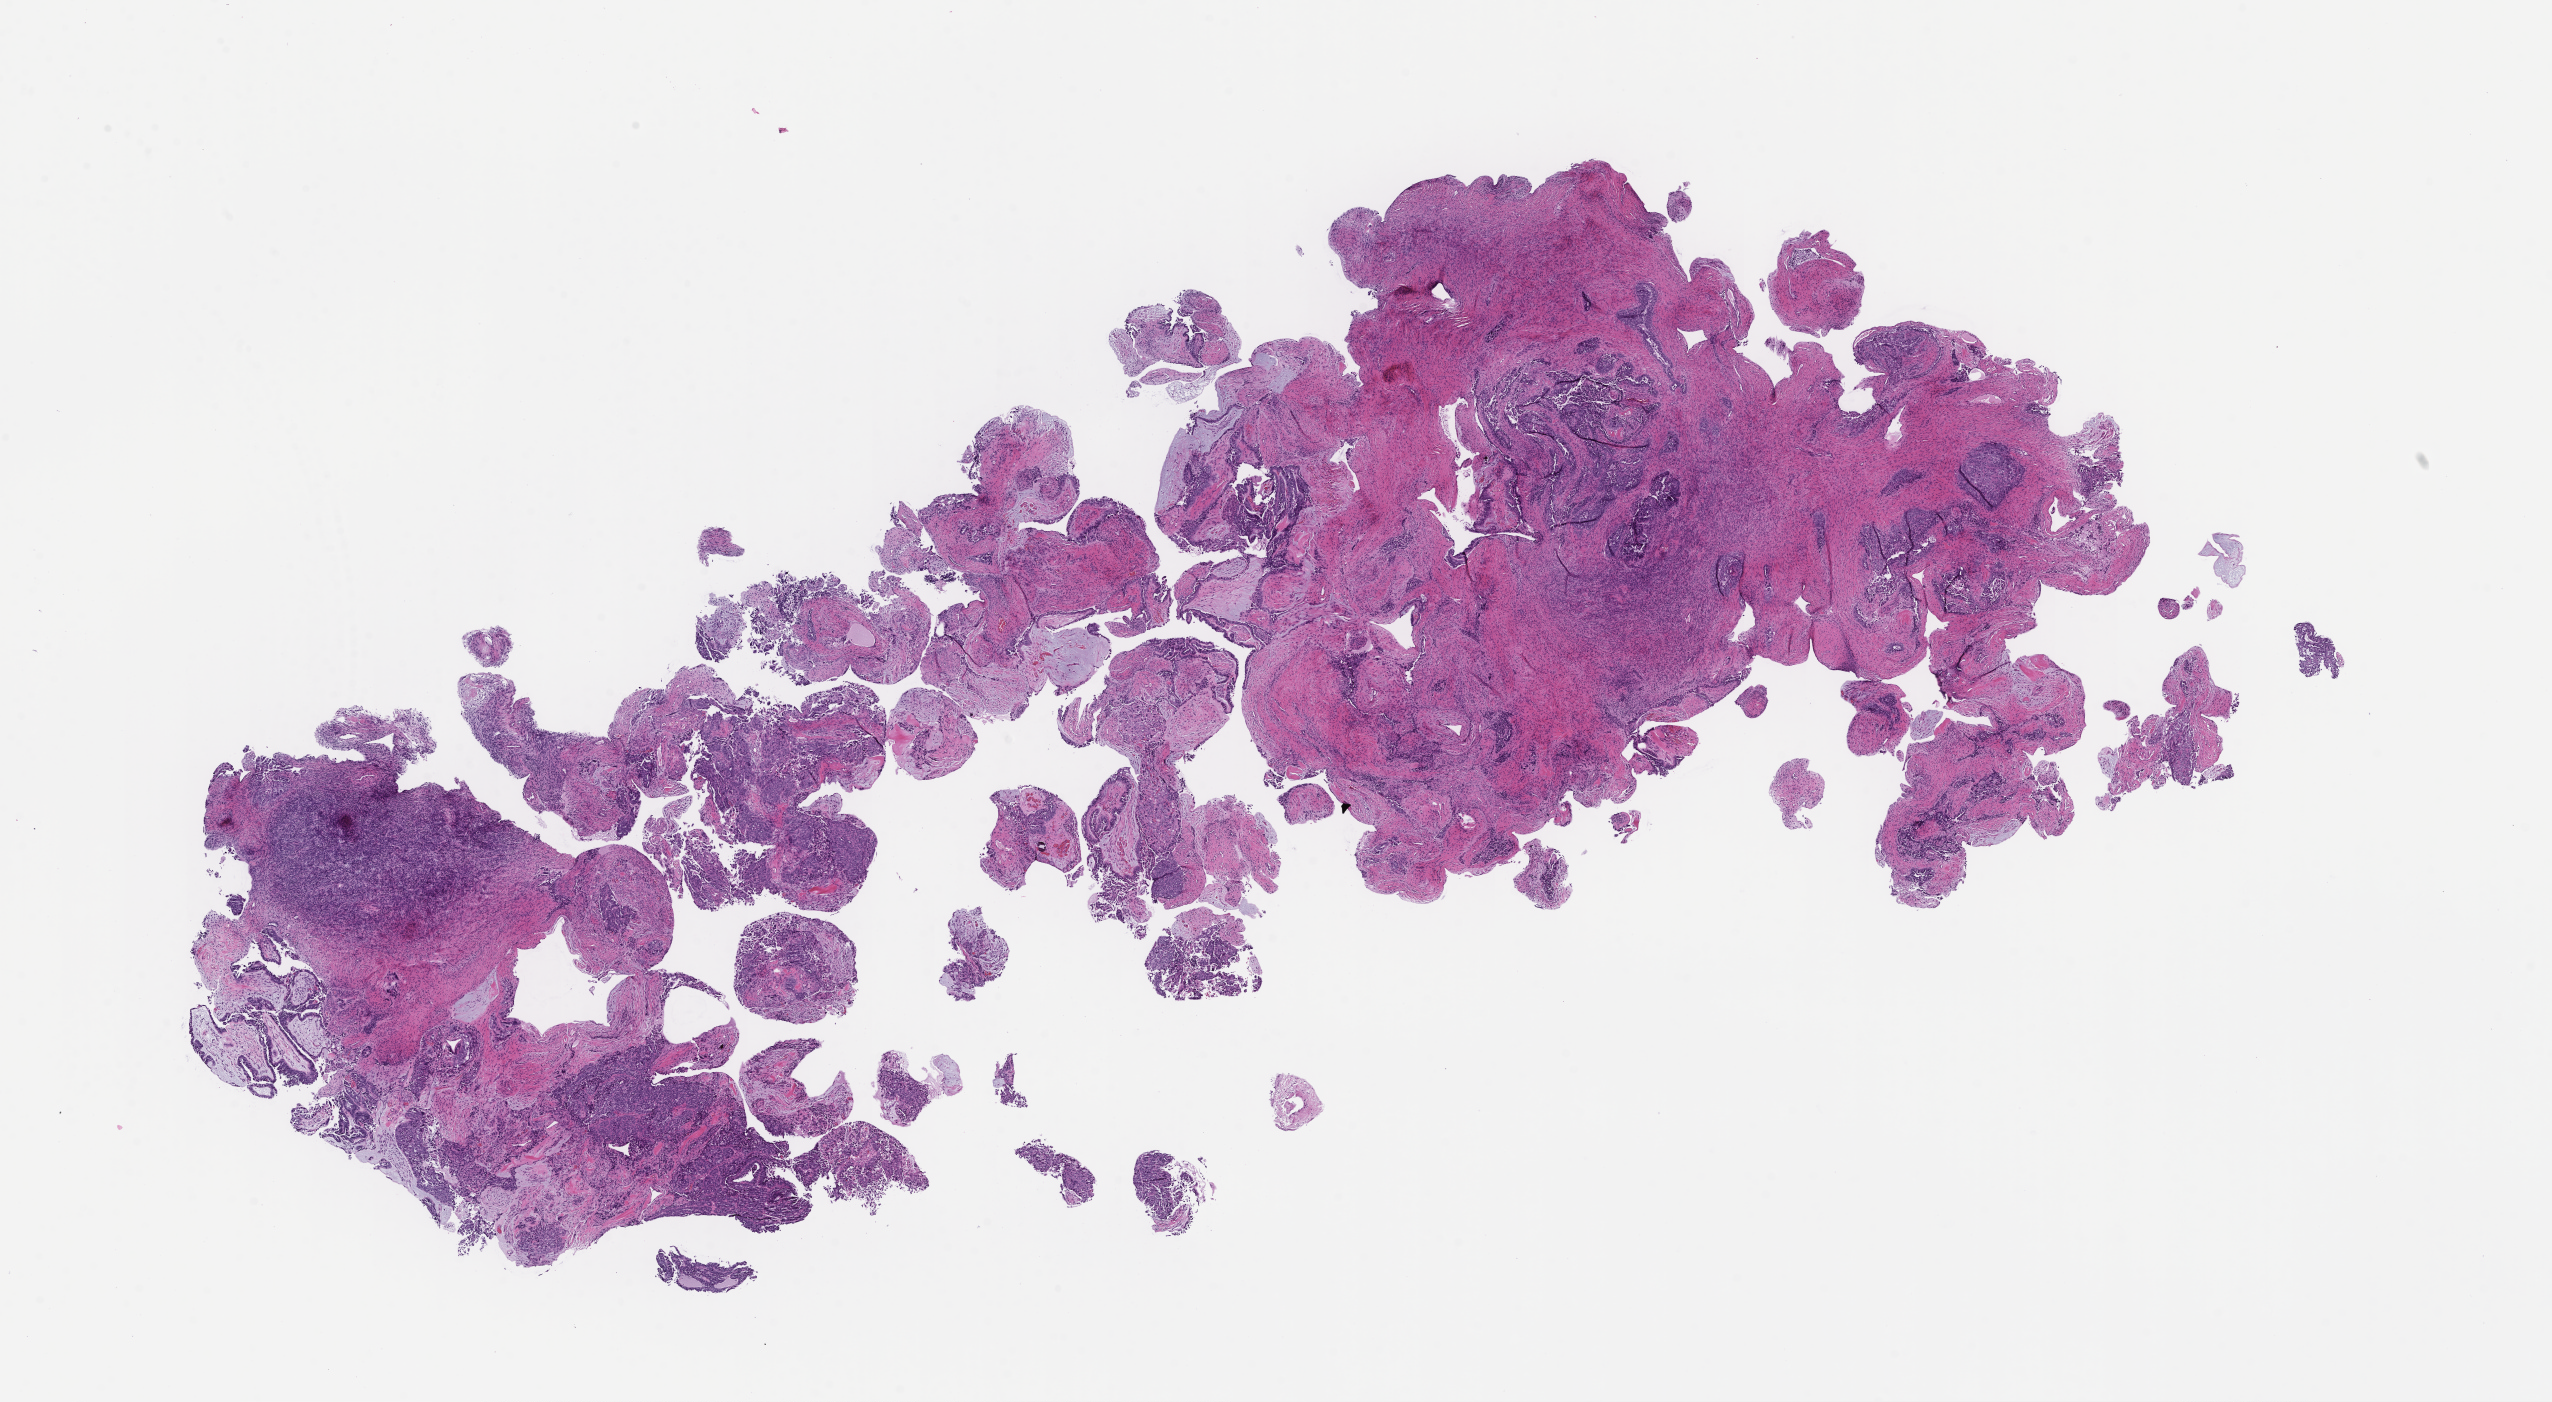
Digitized haematoxylin and eosin-stained section, a low-resolution overview of the entire scanned area, about 20.6 x 11.3 mm. Formalin-fixed, paraffin-embedded (FFPE) tissue. Tissue site: ovary. Collected at baseline (before treatment). Patient: female.
- this section: primary tumour tissue
- diagnosis: Ovarian Carcinoma